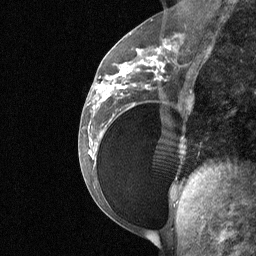
Breast MRI (dynamic contrast-enhanced), one sagittal slice; dynamic contrast-enhanced study with each time point stored as its own series, time point 2 of 3 at this slice position (early post-contrast, ordered by acquisition time); 1.5 T; TE 4.8 ms, TR 27 ms; 2 mm slice thickness; 256 × 256 image matrix, field of view 200 × 200 mm. Female patient, age 34 years. Case-level facts recorded for this patient, not image findings: setting: breast cancer imaged before/during neoadjuvant chemotherapy; receptor status: HR-positive, HER2-negative.
Outlined on this slice (semi-automatically segmented with operator editing):
- analysis volume of interest (the breast-tissue region the enhancement analysis was run in; not a lesion): bounding box (x1, y1, x2, y2) in pixels: (92, 50, 188, 185)
- tumour enhancement mask (voxels above the 90 % enhancement threshold inside the analysis volume of interest): (94, 50, 164, 108)